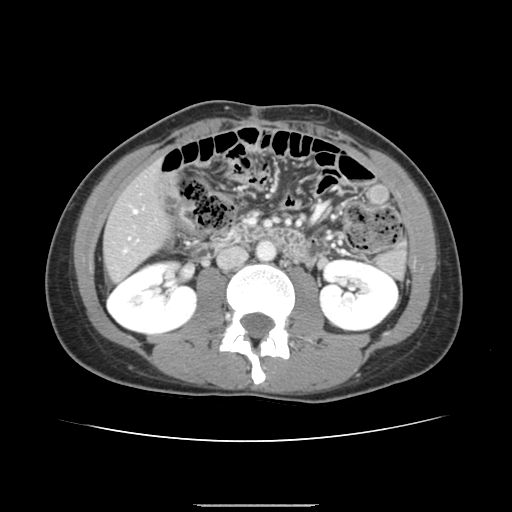
Contrast-enhanced abdominal CT, one axial slice; slice 51 of 150 in the series (ordered by position); intravenous contrast given; soft-tissue window (W 400 / L 40 HU); 512 × 512 image matrix, field of view 324 × 324 mm. Female patient, age 32 years. Case-level facts recorded for this patient, not image findings: diagnosis: colorectal cancer liver metastases, imaged before liver resection; multiple liver metastases: yes; largest metastasis: 0.7 cm; disease in both lobes: no.
Annotated regions visible in this slice (manually delineated by an expert):
- hepatic veins: bounding box <125,210,137,251> (left, top, right, bottom; pixels)
- liver: <105,166,167,280>
- planned liver remnant (the part of the liver to remain after resection): <105,166,167,280>